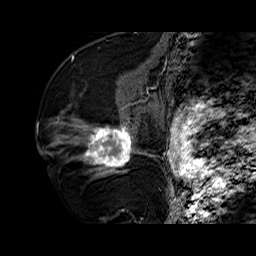
Breast MRI (dynamic contrast-enhanced), one sagittal slice. Slice 34 of 60 in the series (ordered by position). Dynamic contrast-enhanced series, time point 2 of 6 at this slice position (early post-contrast). 1.5 T. TE 6.4 ms, TR 32.7 ms. 4 mm slice thickness. 256 × 256 image matrix. Female patient. Case-level facts recorded for this patient, not image findings: setting: breast cancer imaged before/during neoadjuvant chemotherapy; receptor status: HR-positive, HER2-negative.
Annotated regions visible in this slice (semi-automatic segmentation, software-assisted and operator-edited):
- analysis volume of interest (the breast-tissue region the enhancement analysis was run in; not a lesion): bounding box (x1, y1, x2, y2) in pixels: (73, 110, 141, 177)
- tumour enhancement mask (voxels above the 100 % enhancement threshold inside the analysis volume of interest): (84, 125, 134, 172)